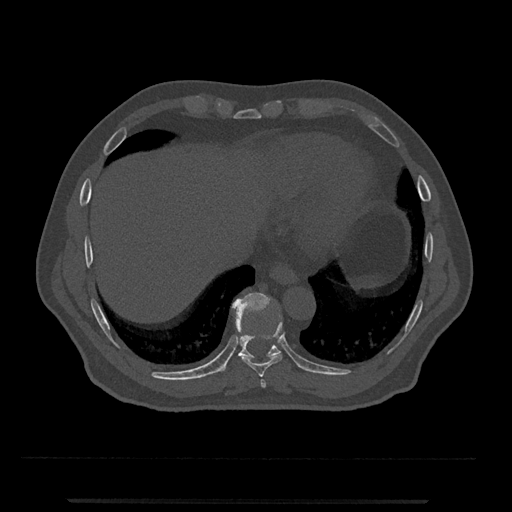
CT including the spine, one axial slice. Position 549 of 797 along the scan axis. 120 kVp. Bone window (W 1800 / L 400 HU). 0.5 mm slice thickness. 512 × 512 image matrix, field of view 419 × 419 mm. Patient: male, 63 years. From the clinical record (not read from this slice): primary cancer: prostate.
Annotated regions visible in this slice (semi-automatic segmentation, software-assisted and operator-edited):
- T10 vertebra: bounding box <219,293,281,372> (left, top, right, bottom; pixels)
- T8 vertebra: <260,379,266,388>
- T9 vertebra: <241,314,283,377>